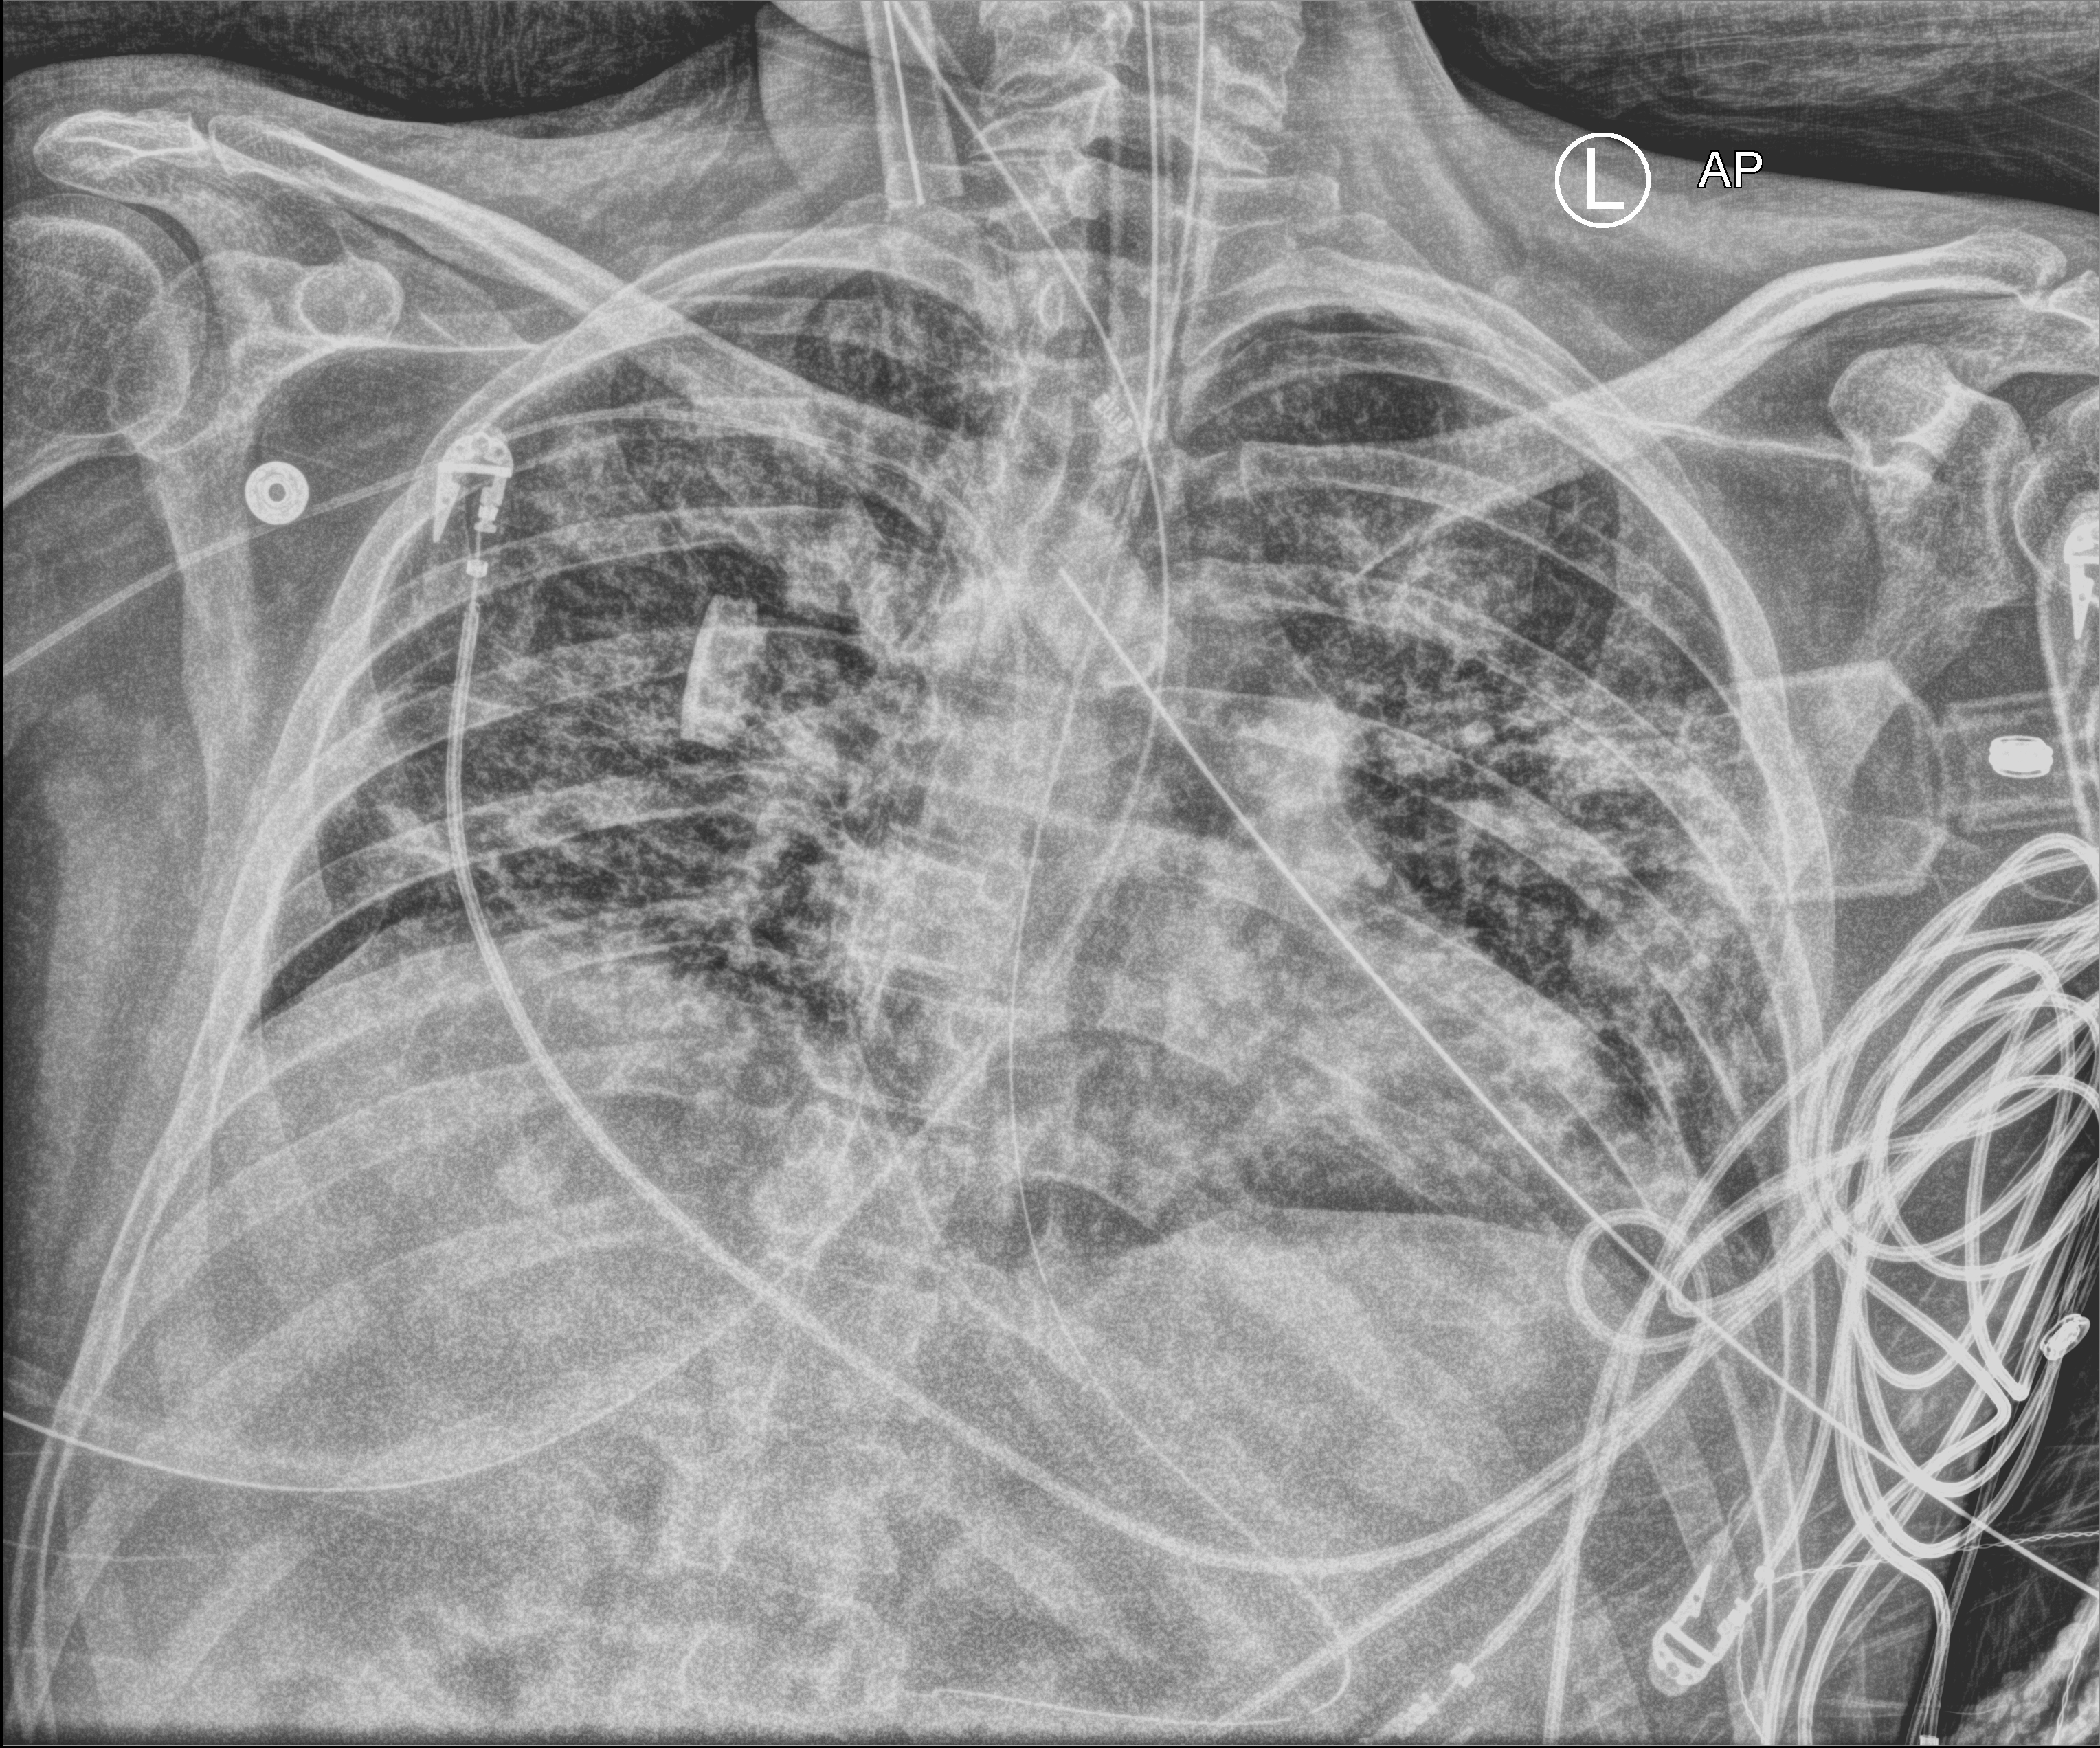
Portable chest radiograph; anteroposterior (AP) projection. Patient hospitalised with COVID-19; male, aged 18–59 years.
Admission-level facts for this patient (not findings on this image; timing relative to this image not recorded):
- admitted to intensive care during this hospital stay: yes